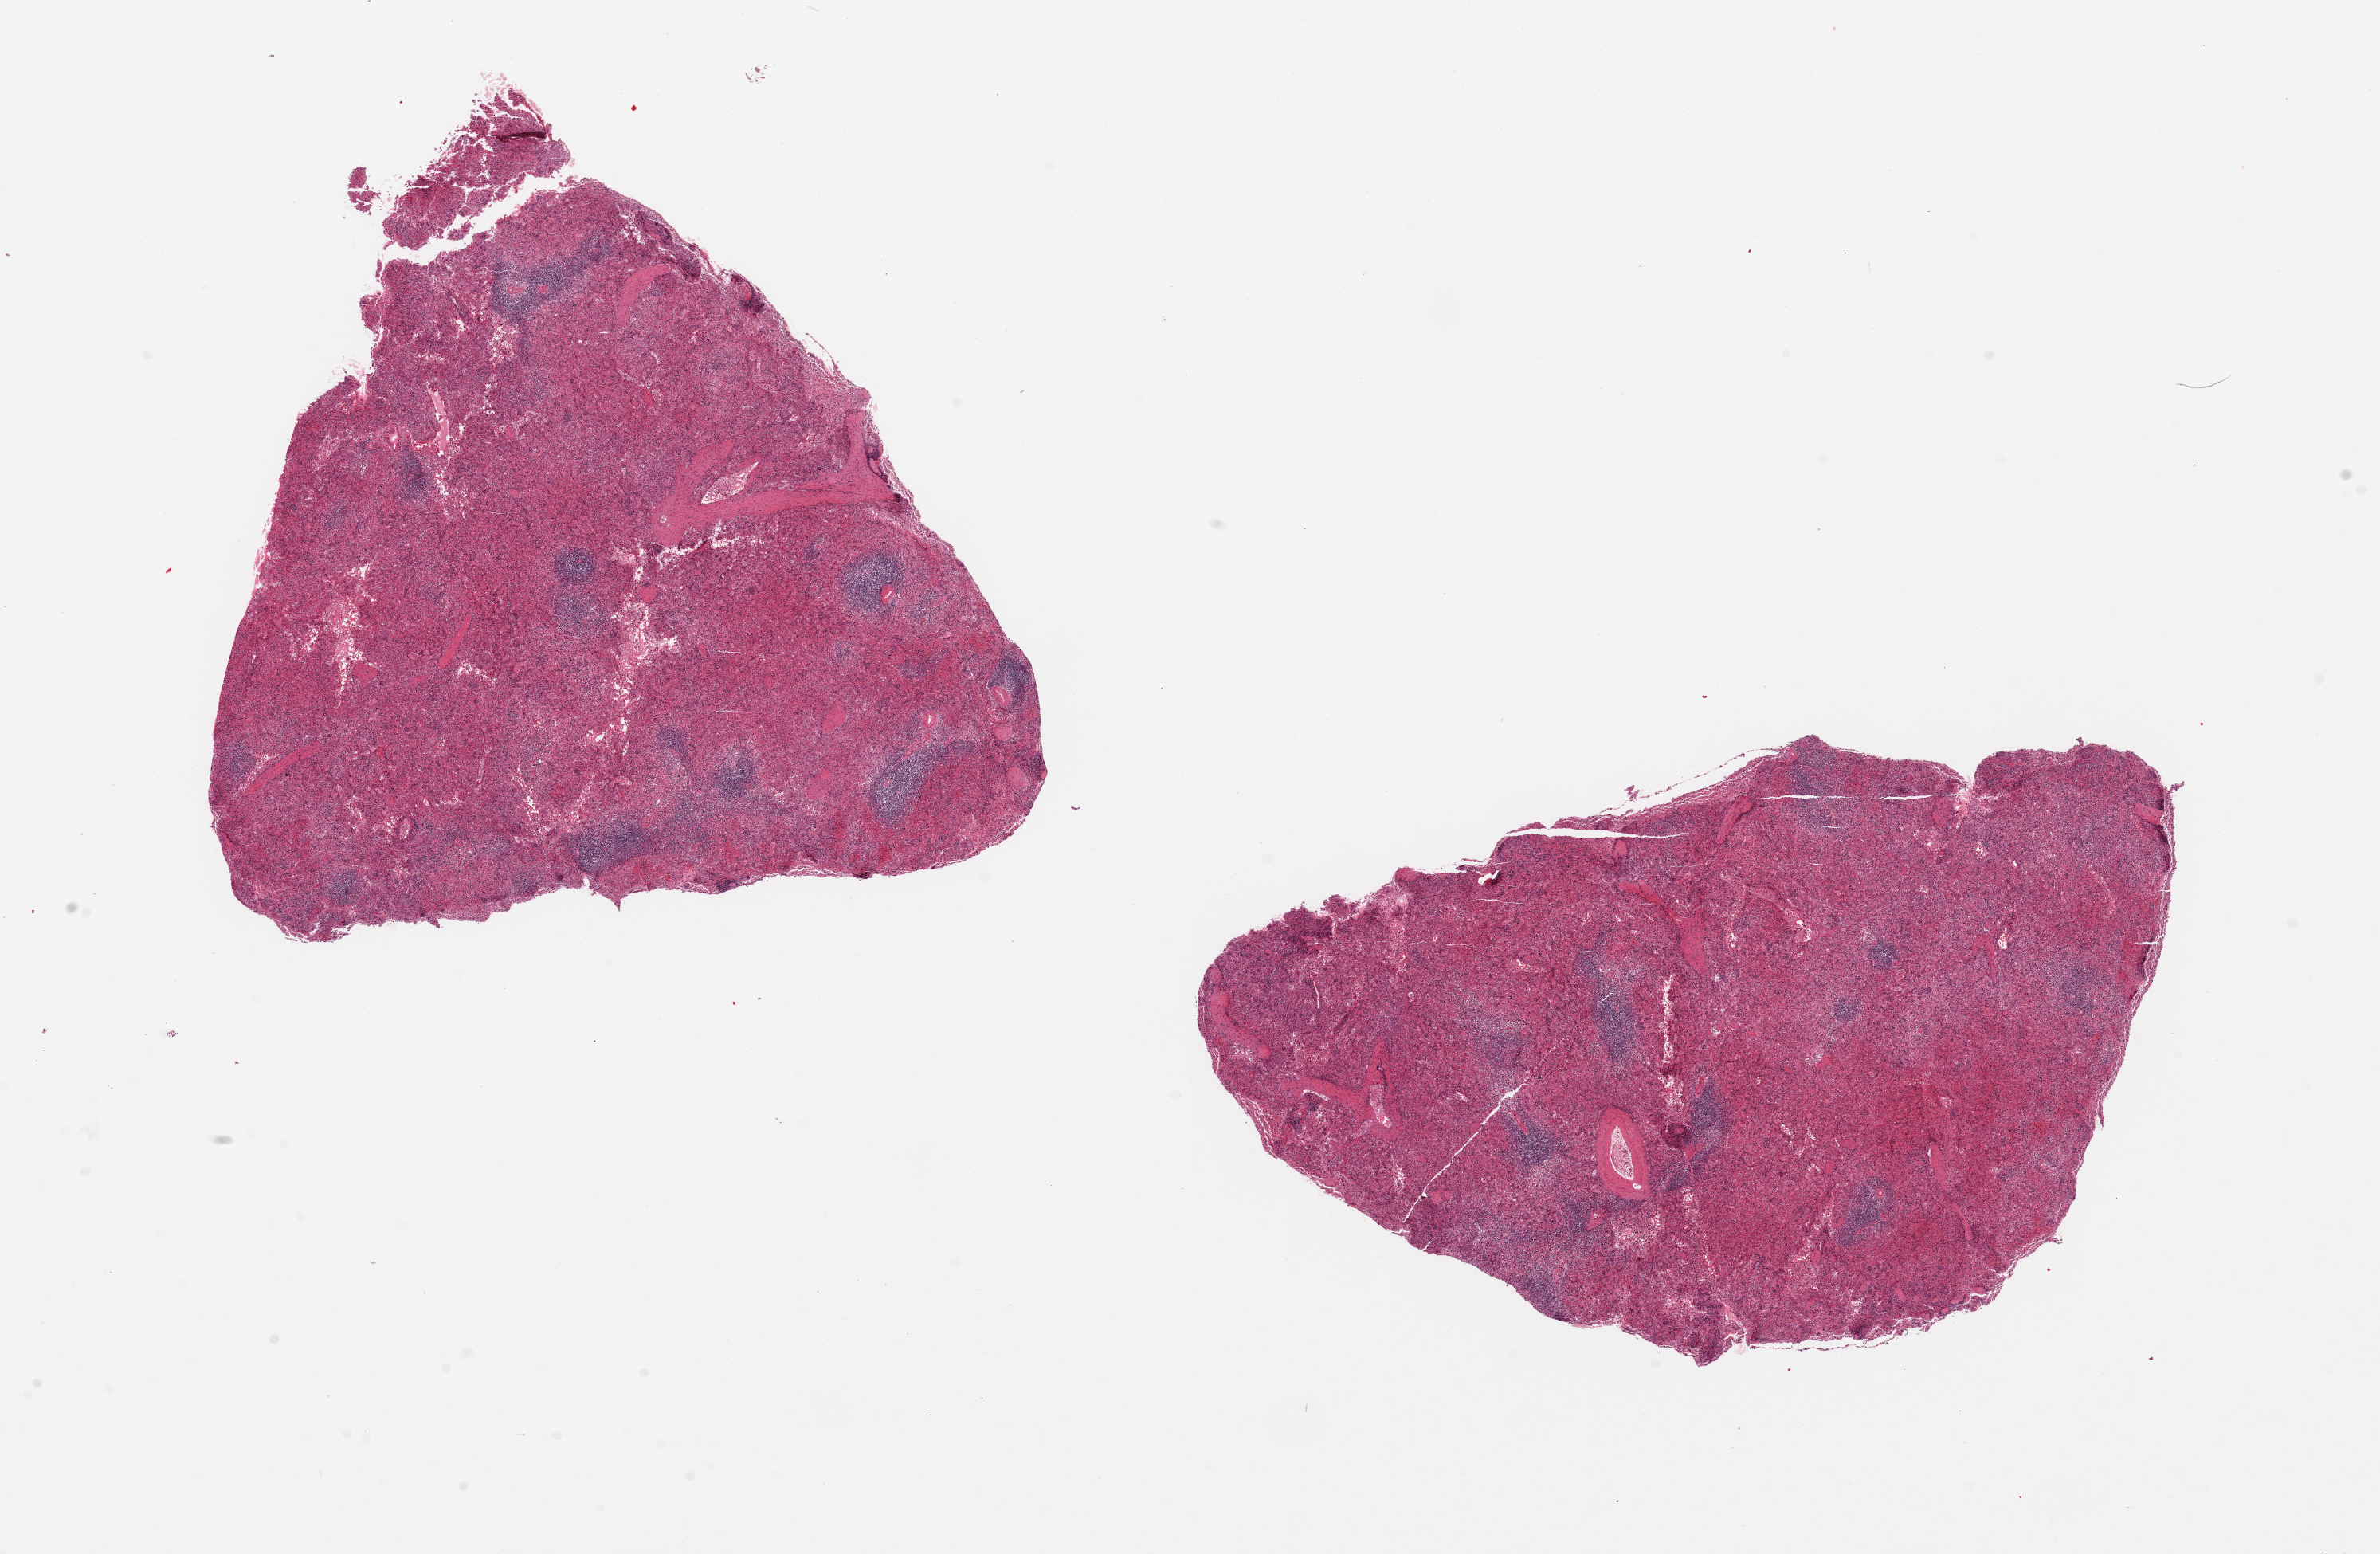
Digitized hematoxylin and eosin (H&E)-stained section, a low-resolution overview of the entire scanned area, about 23.6 x 15.4 mm (acquisition: 20x scan); PAXgene-fixed, paraffin-embedded tissue; target tissue: spleen; donor tissue sample. Donor: male.
Review note (as recorded): 2 pieces 8x8 & 10x6 mm; moderate congestion.